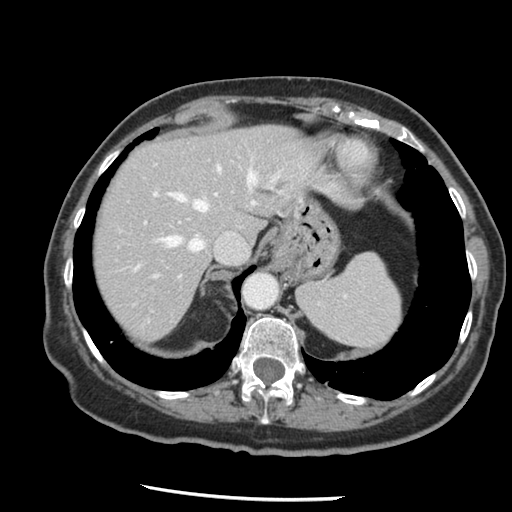
Contrast-enhanced abdominal CT, one axial slice; slice 106 of 148 in the series (ordered by position); 120 kVp; intravenous contrast given; soft-tissue window (W 400 / L 40 HU); 512 × 512 image matrix, field of view 330 × 330 mm. Female patient, age 85 years. Case-level facts recorded for this patient, not image findings: diagnosis: colorectal cancer liver metastases, imaged before liver resection; multiple liver metastases: no; largest metastasis: 0.9 cm; chemotherapy before resection: yes.
Annotated regions visible in this slice (expert manual segmentation):
- hepatic veins: bounding box (x1, y1, x2, y2) in pixels: (135, 151, 285, 270)
- liver: (93, 126, 320, 341)
- planned liver remnant (the part of the liver to remain after resection): (93, 126, 320, 341)
- portal vein (with intrahepatic branches): (145, 160, 219, 279)